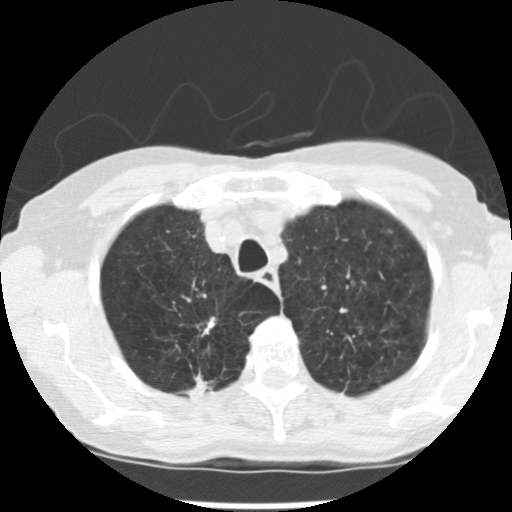
Chest CT (low-dose screening protocol), one axial image; first (baseline) screen; lung window (W 1500 / L -600 HU); standard (soft-tissue) reconstruction kernel (STANDARD); slice 43 of 265 in the series. Female participant, aged 72 years at enrolment. Current smoker at enrolment.
2 expert reader's lesion annotations on this slice (largest first), bounding box [x1, y1, x2, y2] px = [182, 368, 229, 406]; [187, 309, 231, 345]. The screening reader recorded 3 non-calcified nodules or masses ≥4 mm on this exam (right upper lobe, left upper lobe, left lower lobe); which of them these boxes mark is not recorded. Official screen result: positive, change unspecified: nodule(s) >= 4 mm or enlarging nodule(s), mass(es), or other non-specific abnormalities suspicious for lung cancer. Lung cancer was diagnosed 50 days after this screen: adenocarcinoma, NOS, right upper lobe, moderately differentiated (G2), stage IB (AJCC 6th edition), 22 mm at pathology.